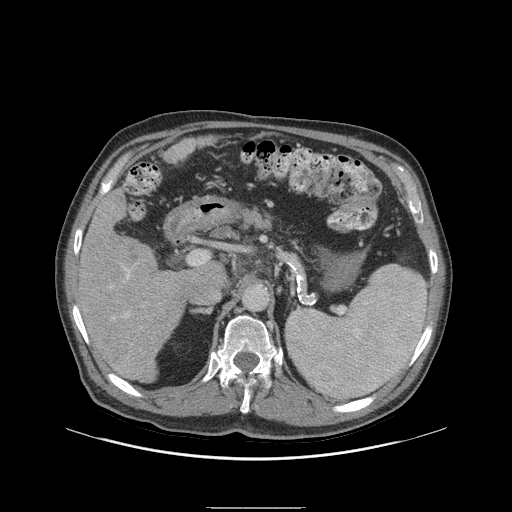
Contrast-enhanced abdominal CT (liver protocol), one axial slice. Slice 52 of 105 in the series (ordered by position). Reconstruction kernel STANDARD. 140 kVp. Soft-tissue window (W 400 / L 40 HU). 2.5 mm slice thickness. 512 × 512 image matrix, field of view 440 × 440 mm. From the clinical record (not read from this slice): diagnosis: hepatocellular carcinoma (patient treated with transarterial chemoembolisation; whether this scan precedes or follows treatment is not stated here); TNM stage (as recorded): Stage-I; Child-Pugh class: A; tumour nodularity: uninodular.
Structures marked on this image (semi-automatically segmented with operator editing):
- liver parenchyma outside the tumour (the mass and vessels are separate outlines, so this box may not span the whole liver): bounding box <74,189,194,382> (left, top, right, bottom; pixels)
- liver vessels: <112,265,131,320>